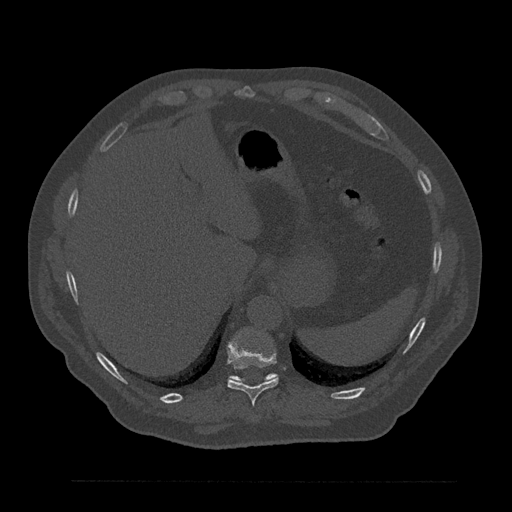
CT including the spine, one axial slice. Position 335 of 797 along the scan axis. 120 kVp. Bone window (W 1800 / L 400 HU). 0.5 mm slice thickness. 512 × 512 image matrix, field of view 430 × 430 mm. Male patient, age 61 years. Case-level facts recorded for this patient, not image findings: primary cancer: prostate.
Annotated regions visible in this slice (semi-automatically segmented with operator editing):
- T10 vertebra: bounding box <227,338,279,406> (left, top, right, bottom; pixels)
- T11 vertebra: <229,373,277,382>